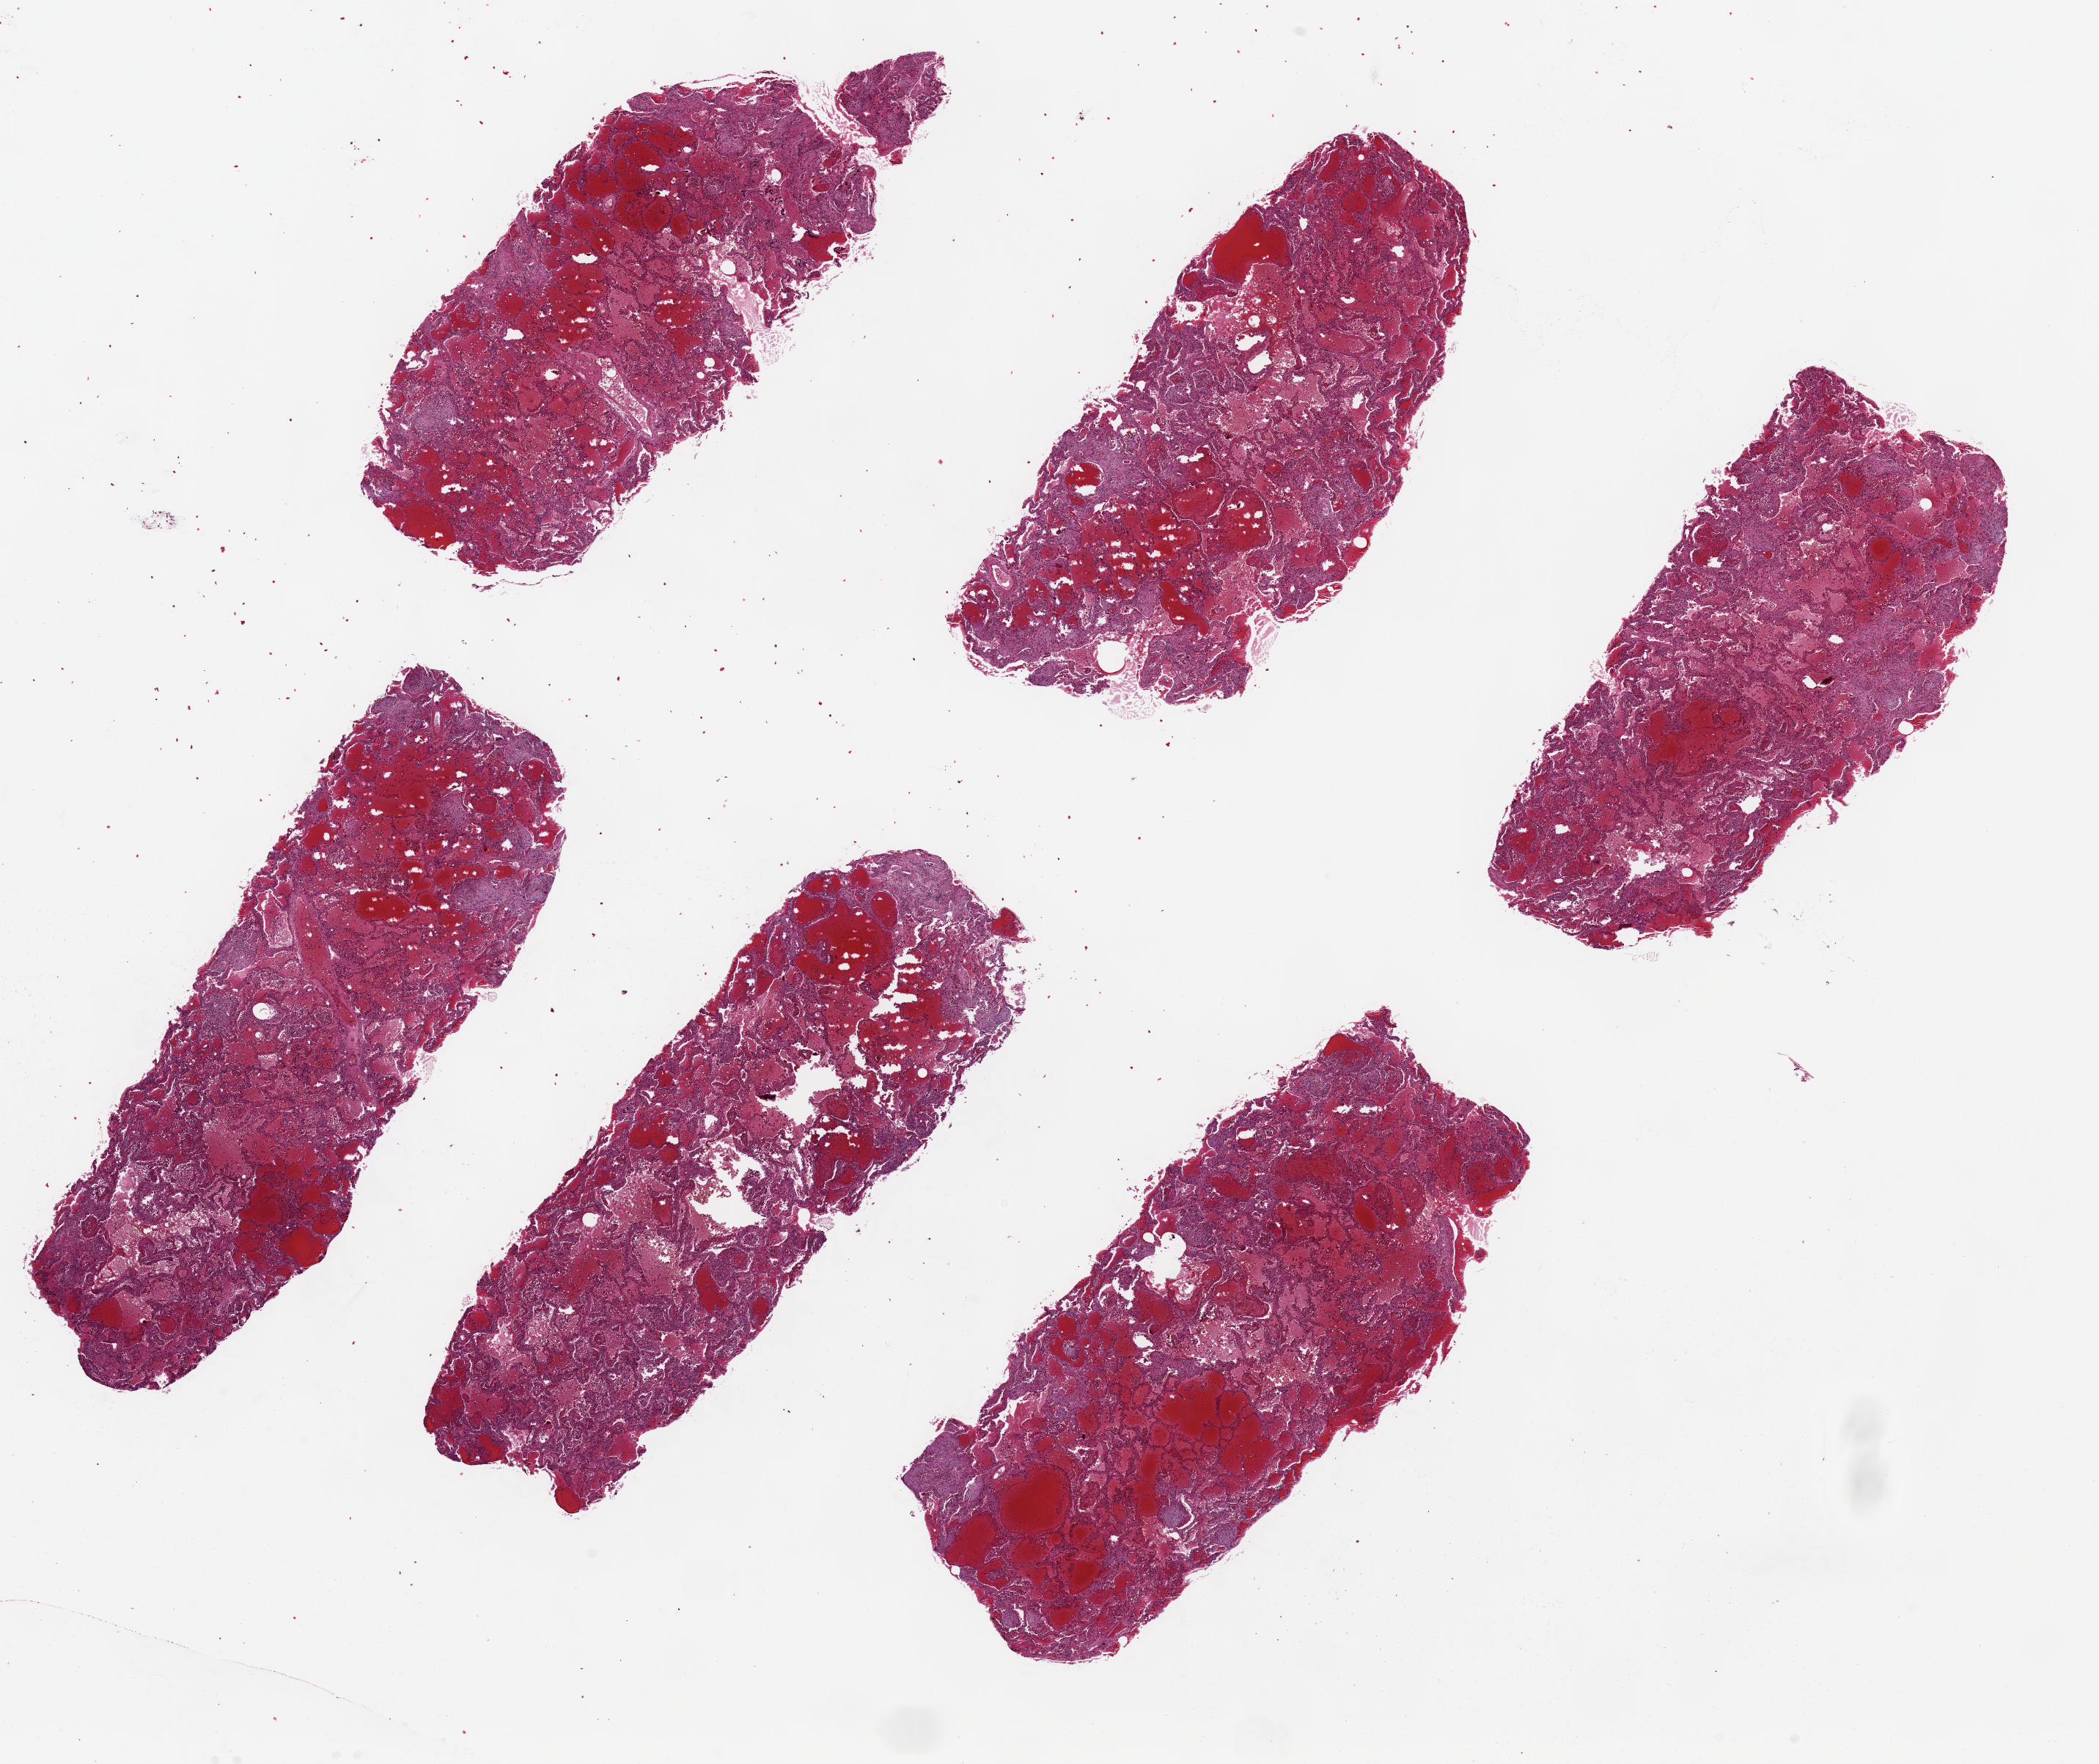
Digitized hematoxylin and eosin (H&E)-stained section — a low-resolution overview of the entire scanned area, about 22.6 x 19.0 mm (slide scanned at 20x). PAXgene-fixed, paraffin-embedded tissue. Target tissue: lung. Tissue donor sample. Donor: male.
Review note (as recorded): 6 pieces up to 8.3x3.4 mm with severe interstitial and alveolar fibrosis & severe hemorrhage.